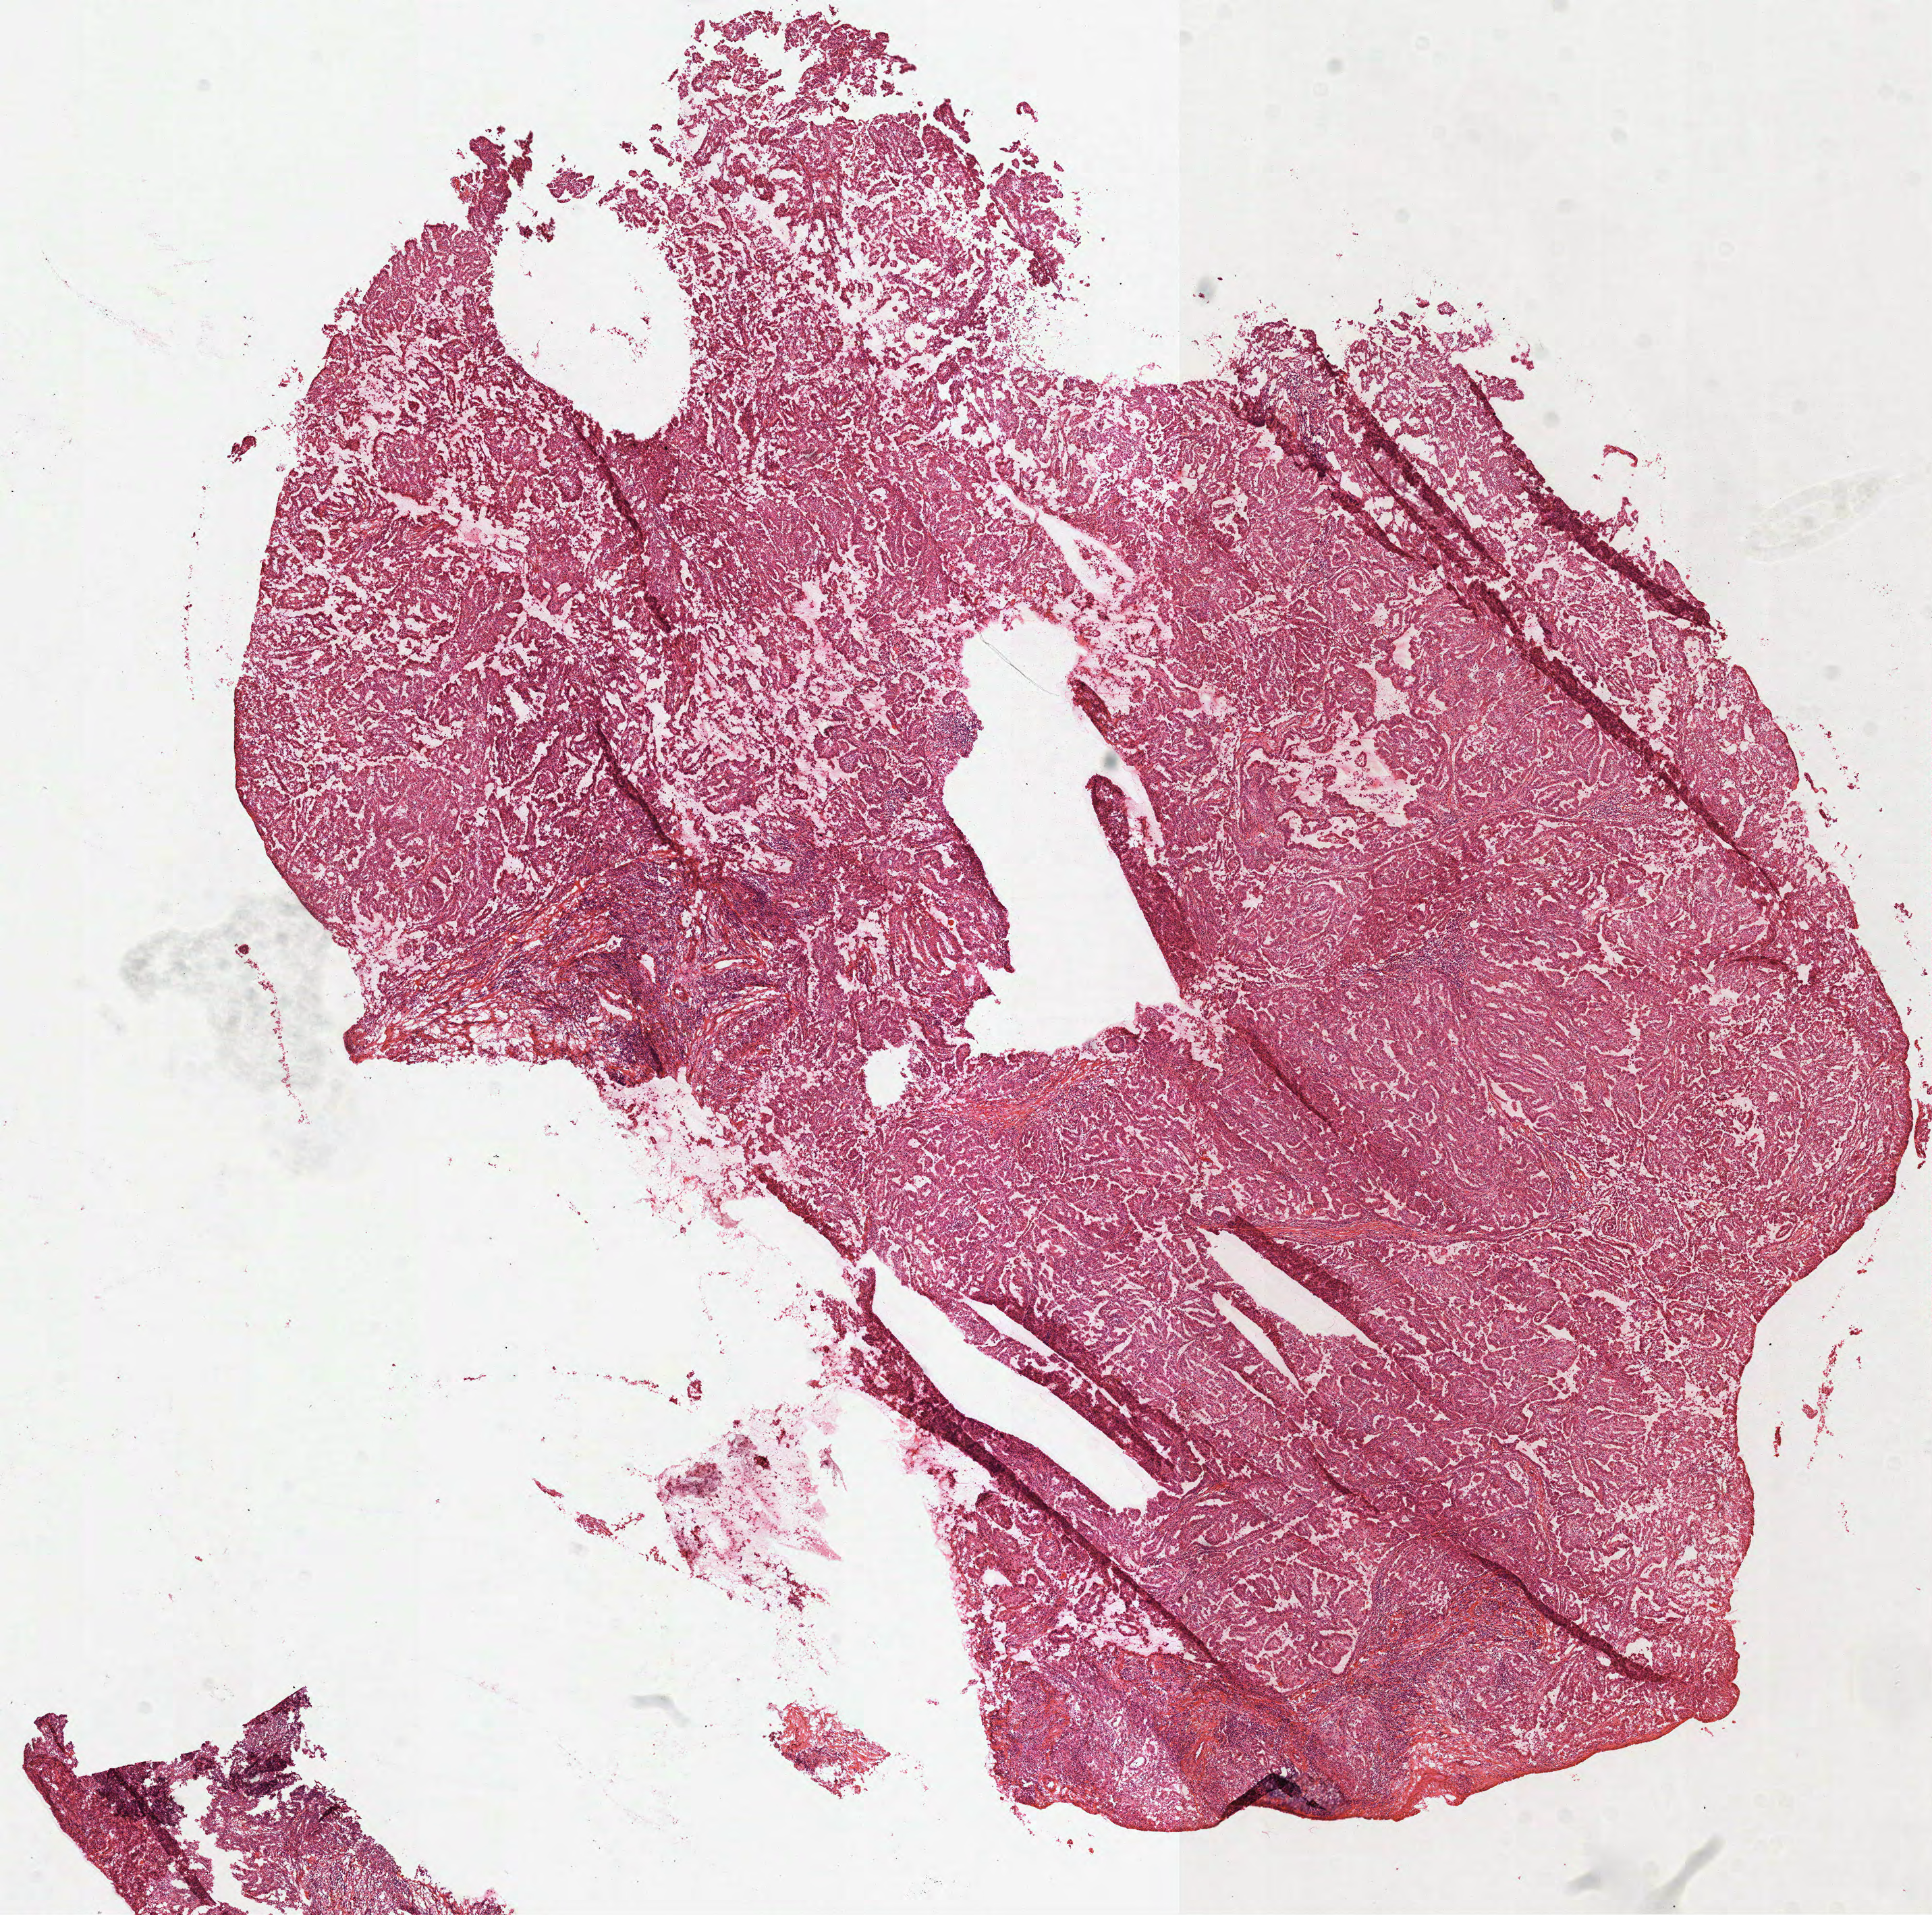
Whole-slide histology image, Hematoxylin and eosin (H&E) stained, shown as a low-resolution overview of the whole scanned area (about 11.5 x 11.4 mm); frozen section from the top of the tissue portion; primary tumour sample from the kidney. Patient: female, age at initial diagnosis 37 years. Composition of this section per pathologist review: tumour cells 90%, tumour nuclei 85%, normal cells 0%, stromal cells 10%, necrosis 0%.
Diagnosis: Papillary adenocarcinoma, NOS. Laterality: left. TNM: T3 N1 M0. Lymph nodes positive (case pathology): 2 of 2 examined. AJCC pathologic stage: III (7th edition).